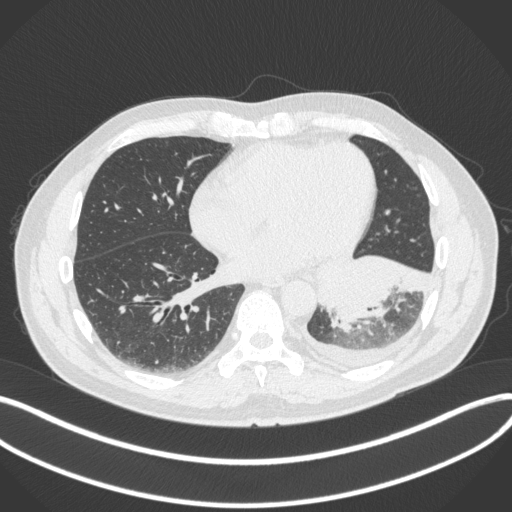
Chest CT, one axial slice. Slice 132 of 350 in the series (ordered by position). Reconstruction kernel B31f. 120 kVp. Lung window (W 1500 / L -600 HU). 512 × 512 image matrix, field of view 400 × 400 mm. Male patient, age 58 years. From the clinical record (not read from this slice): clinical TNM (as recorded): T3 N1 M1b.
Outlined on this slice (rectangle marked by the reading radiologist):
- lung tumour (recorded histology: small cell carcinoma): bounding box <312,253,432,331> (left, top, right, bottom; pixels)